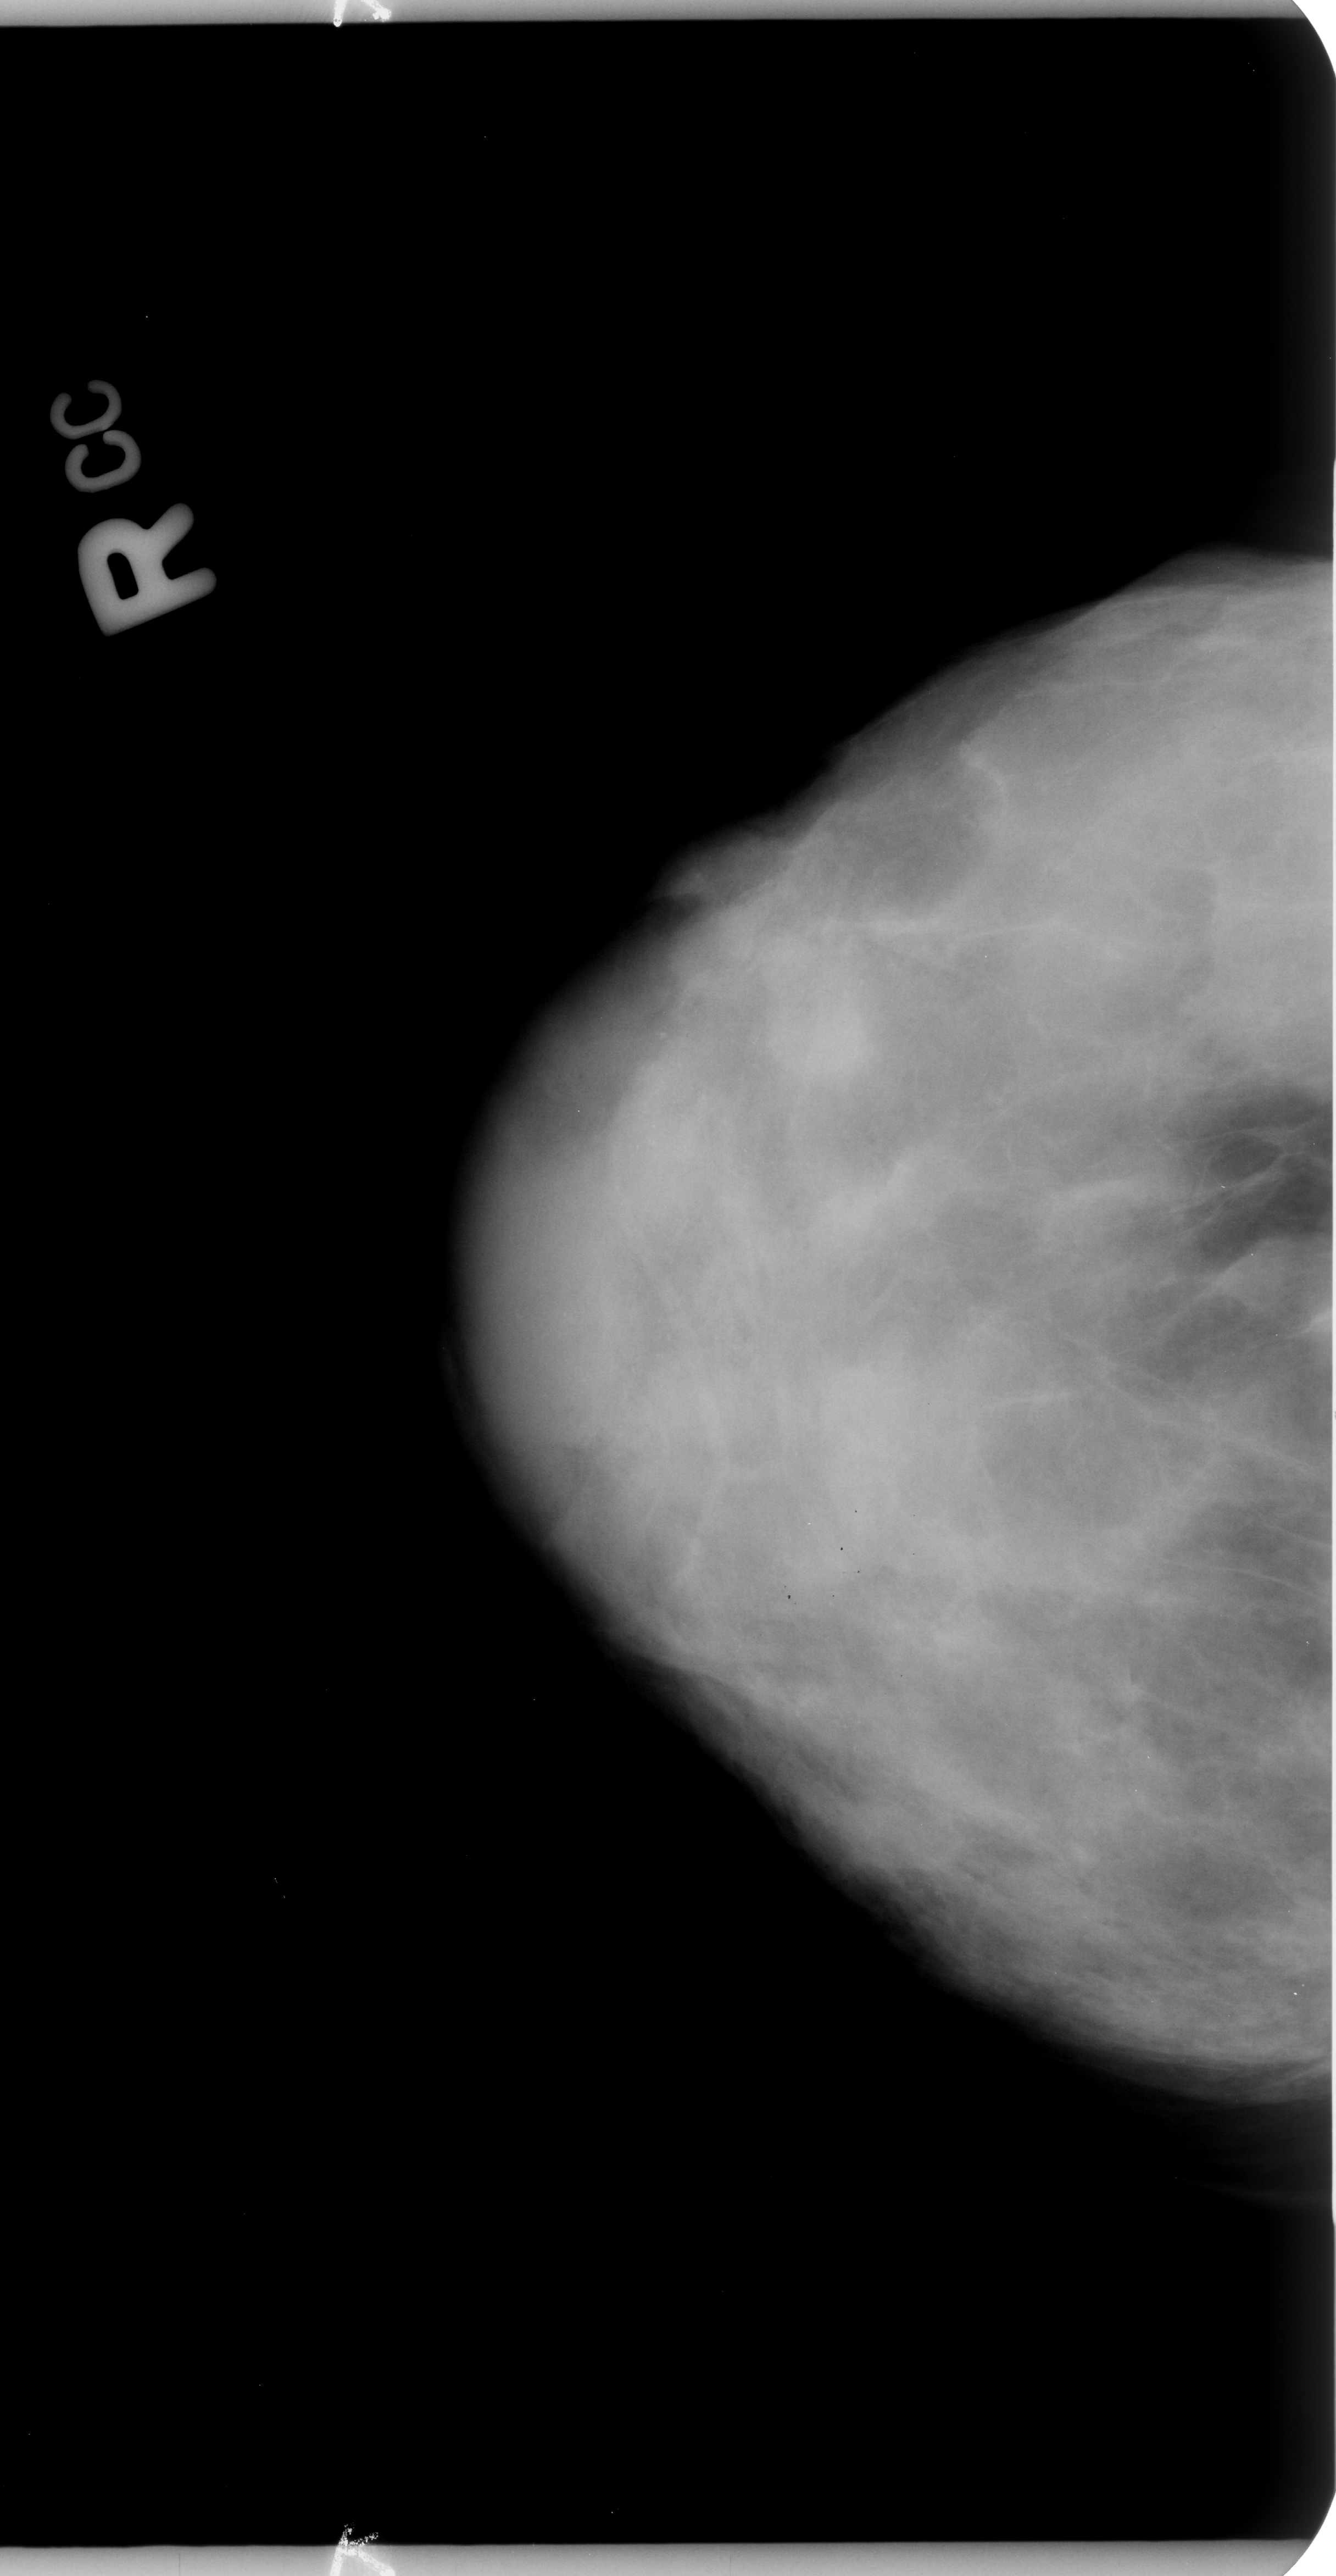
Scanned film-screen mammogram, right breast, CC view, BI-RADS breast density category 4 (scale 1–4).
Marked findings (only marked abnormalities are described; nothing is implied about the rest of the image): calcifications, morphology pleomorphic, distribution regional; BI-RADS assessment category 4; subtlety rating 3 on a 1 (subtle) to 5 (obvious) scale; pathology (as recorded): benign.